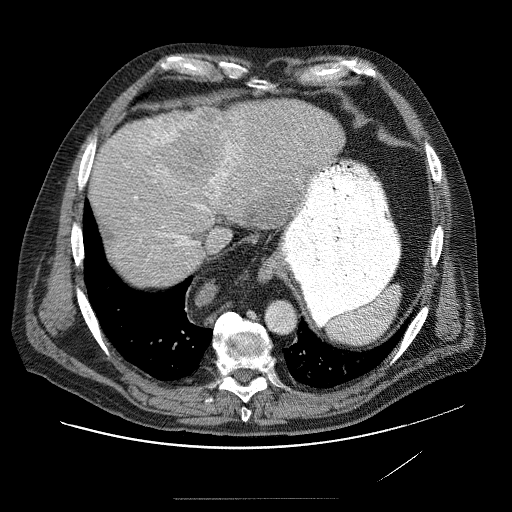
Contrast-enhanced abdominal CT (liver protocol), one axial slice. Position 67 of 89 along the scan axis. Reconstruction kernel STANDARD. Soft-tissue window (W 400 / L 40 HU). 2.5 mm slice thickness. 512 × 512 image matrix, field of view 420 × 420 mm. From the clinical record (not read from this slice): diagnosis: hepatocellular carcinoma (patient treated with transarterial chemoembolisation; whether this scan precedes or follows treatment is not stated here); TNM stage (as recorded): Stage-IVA; Child-Pugh class: A; tumour differentiation: moderately differentiated.
Outlined on this slice (semi-automatic segmentation, software-assisted and operator-edited):
- liver parenchyma outside the tumour (the mass and vessels are separate outlines, so this box may not span the whole liver): bounding box <90,102,342,274> (left, top, right, bottom; pixels)
- mass: <136,111,301,222>
- liver vessels: <127,119,229,248>